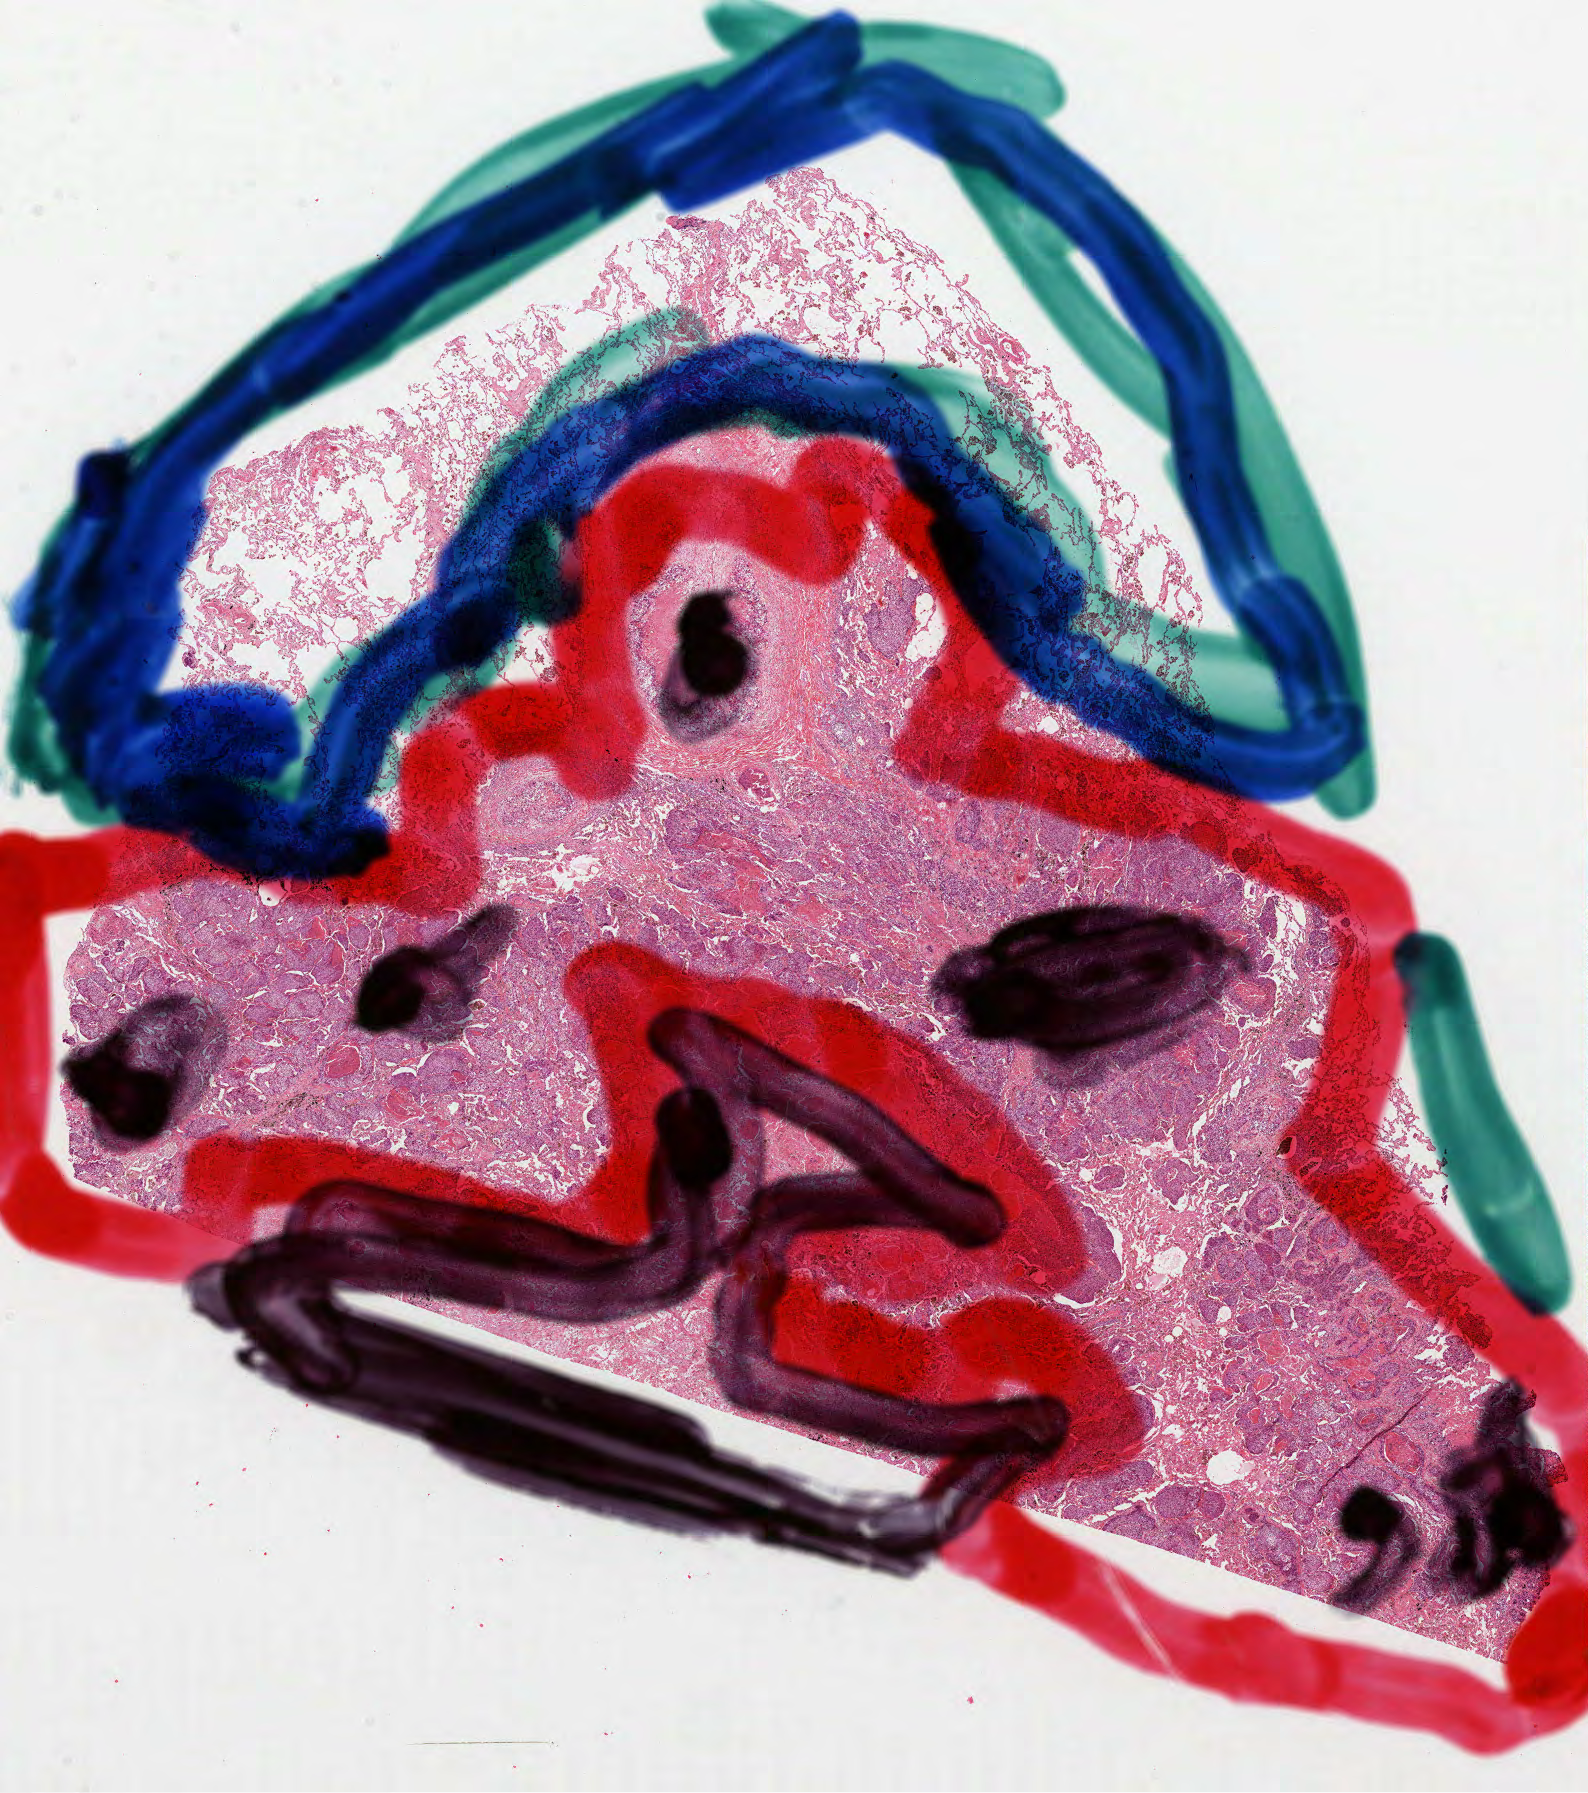
Hematoxylin and eosin (H&E) stained whole-slide image — a low-resolution overview of the entire scanned area, about 12.8 x 14.5 mm (slide scanned at 40x); formalin-fixed paraffin-embedded (FFPE) diagnostic section; sample: primary tumour, lung. Male patient; age at initial diagnosis 53 years.
AJCC pathologic stage: IIB. Laterality: right. Pathologic diagnosis: Squamous cell carcinoma, NOS.